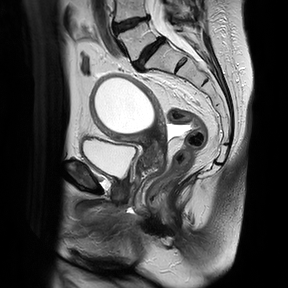
Pelvic MRI for cervical cancer, one sagittal slice; slice 17 of 30 in the series (ordered by position); T2-weighted; 1.5 T; TE 100 ms, TR 4816.3 ms; 4 mm slice thickness; 288 × 288 image matrix, field of view 300 × 300 mm. Patient: female, 74 years.
Annotated regions visible in this slice (manually delineated by an expert):
- uterus and cervix: bounding box [x1, y1, x2, y2] px = [89, 72, 168, 183]